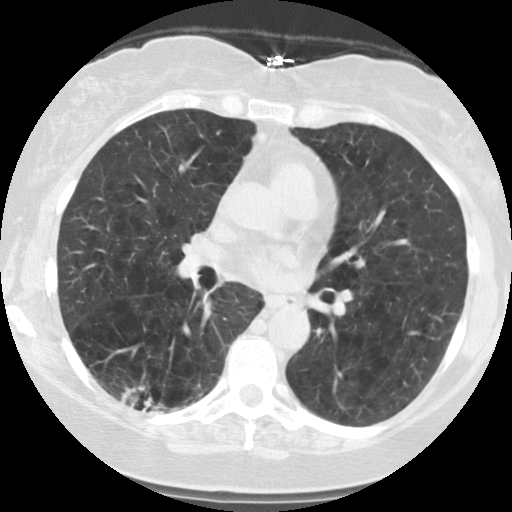
Low-dose screening chest CT, one axial slice. Slice 60 of 122 in the series (ordered by position). Reconstruction kernel STANDARD. 140 kVp. Lung window (W 1500 / L -600 HU). 2.5 mm slice thickness. 512 × 512 image matrix, field of view 310 × 310 mm.
Annotated regions visible in this slice (expert manual segmentation):
- lesion 1 (tumor, lower lobe of right lung): box from (x=121, y=387) to (x=155, y=409) px